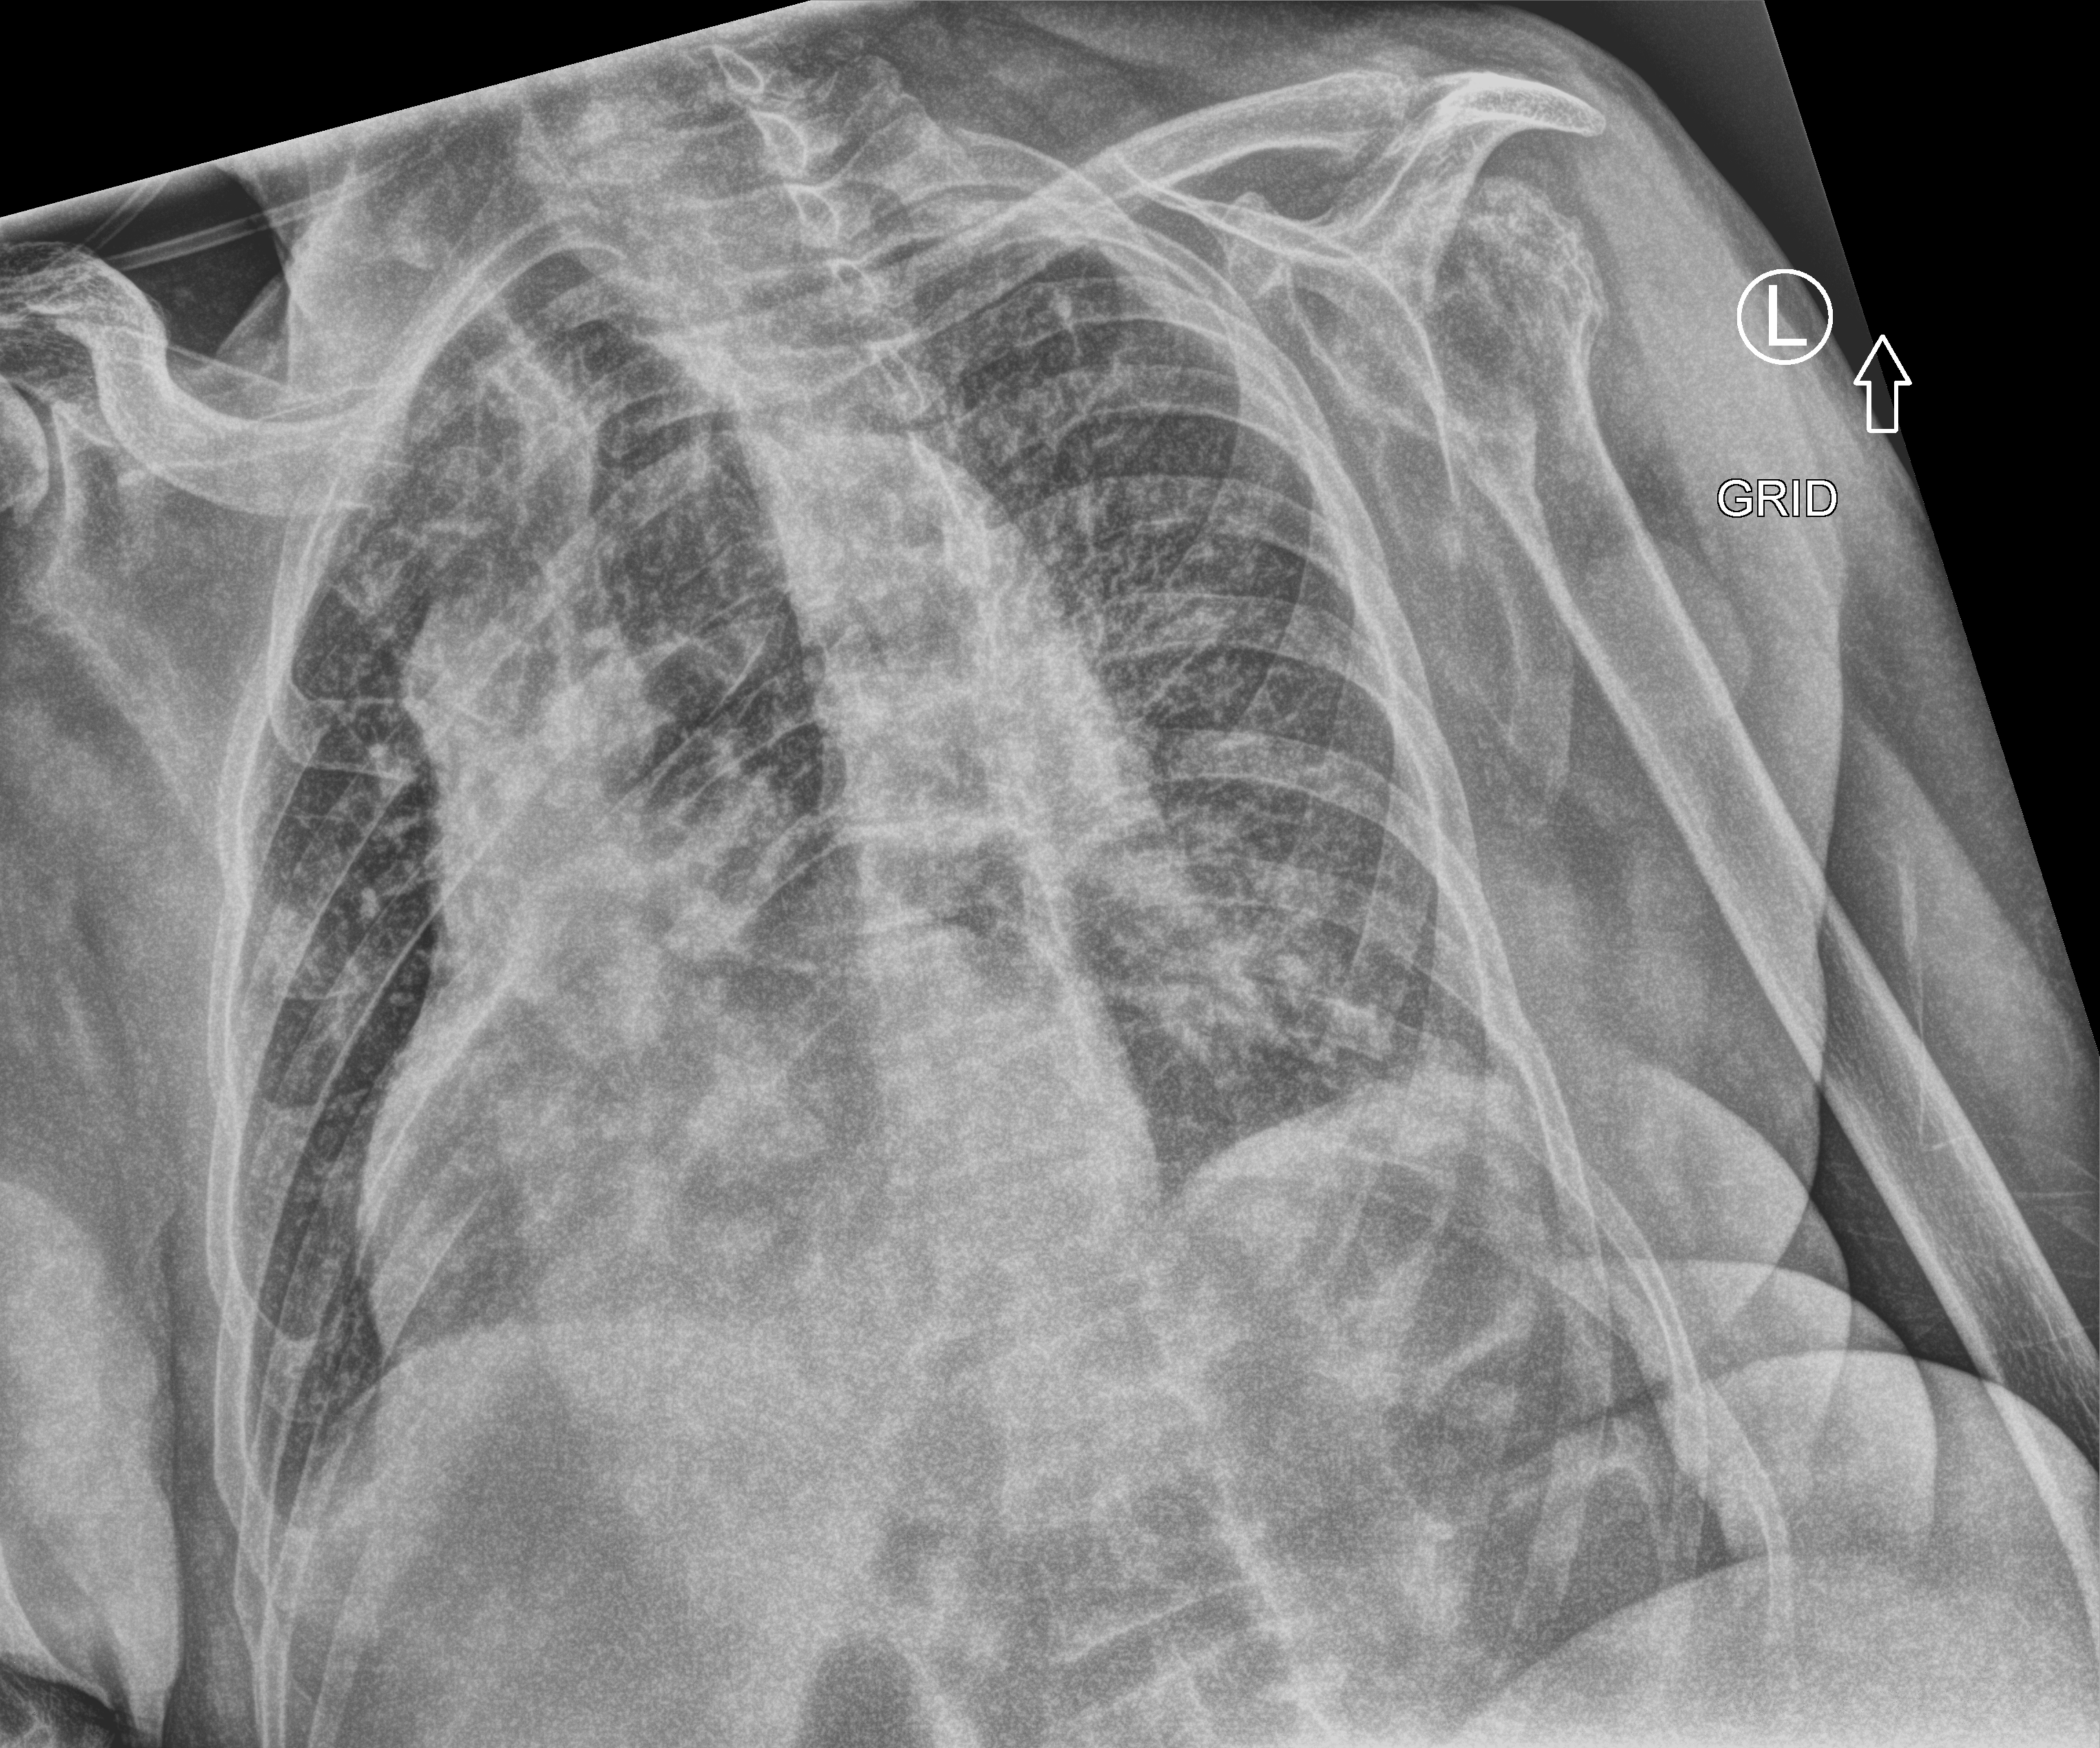
Chest X-ray (portable); anteroposterior (AP) projection. Patient hospitalised with COVID-19; male, aged 75–90 years.
From the hospital-stay record, not from the radiograph (when in the stay this image was taken is not recorded): admitted to intensive care during this hospital stay: no.